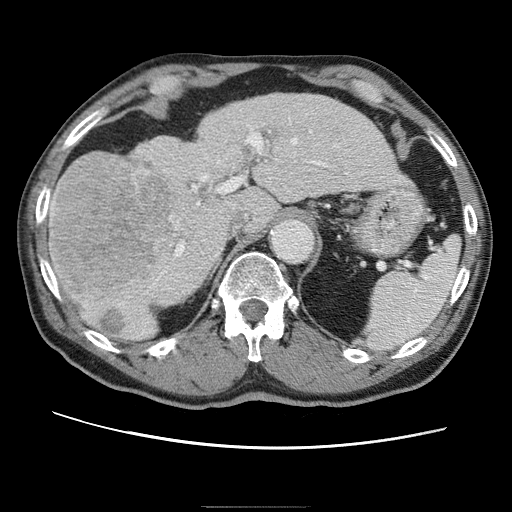
Contrast-enhanced abdominal CT (liver protocol), one axial slice; slice 38 of 75 in the series (ordered by position); 120 kVp; one of 2 acquisitions stored at this slice position; soft-tissue window (W 400 / L 40 HU); 2.5 mm slice thickness; 512 × 512 image matrix. From the clinical record (not read from this slice): diagnosis: hepatocellular carcinoma (patient treated with transarterial chemoembolisation; whether this scan precedes or follows treatment is not stated here); TNM stage (as recorded): Stage-II; Child-Pugh class: A; tumour differentiation: well differentiated.
Annotated regions visible in this slice (semi-automatically segmented with operator editing):
- liver parenchyma outside the tumour (the mass and vessels are separate outlines, so this box may not span the whole liver): bounding box (x1, y1, x2, y2) in pixels: (50, 94, 398, 338)
- mass: (49, 156, 173, 302)
- liver vessels: (79, 127, 353, 311)